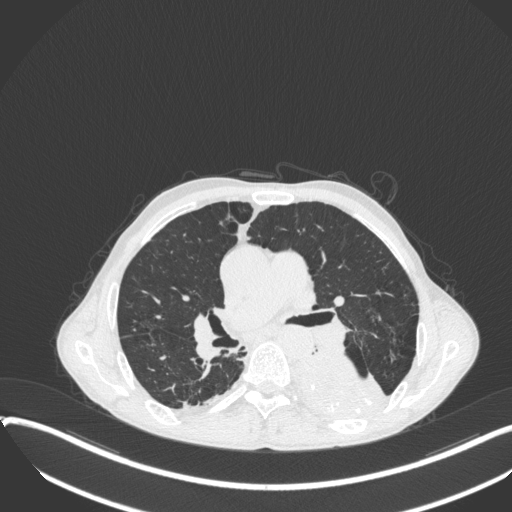
Chest CT, one axial slice. Position 218 of 400 along the scan axis. Reconstruction kernel B31f. 120 kVp. Lung window (W 1500 / L -600 HU). 512 × 512 image matrix, field of view 400 × 400 mm. Patient: male, 57 years. From the clinical record (not read from this slice): clinical TNM (as recorded): T4 N0 M0.
Structures marked on this image (rectangle marked by the reading radiologist):
- lung tumour (recorded histology: squamous cell carcinoma): bounding box (x1, y1, x2, y2) in pixels: (287, 346, 394, 425)